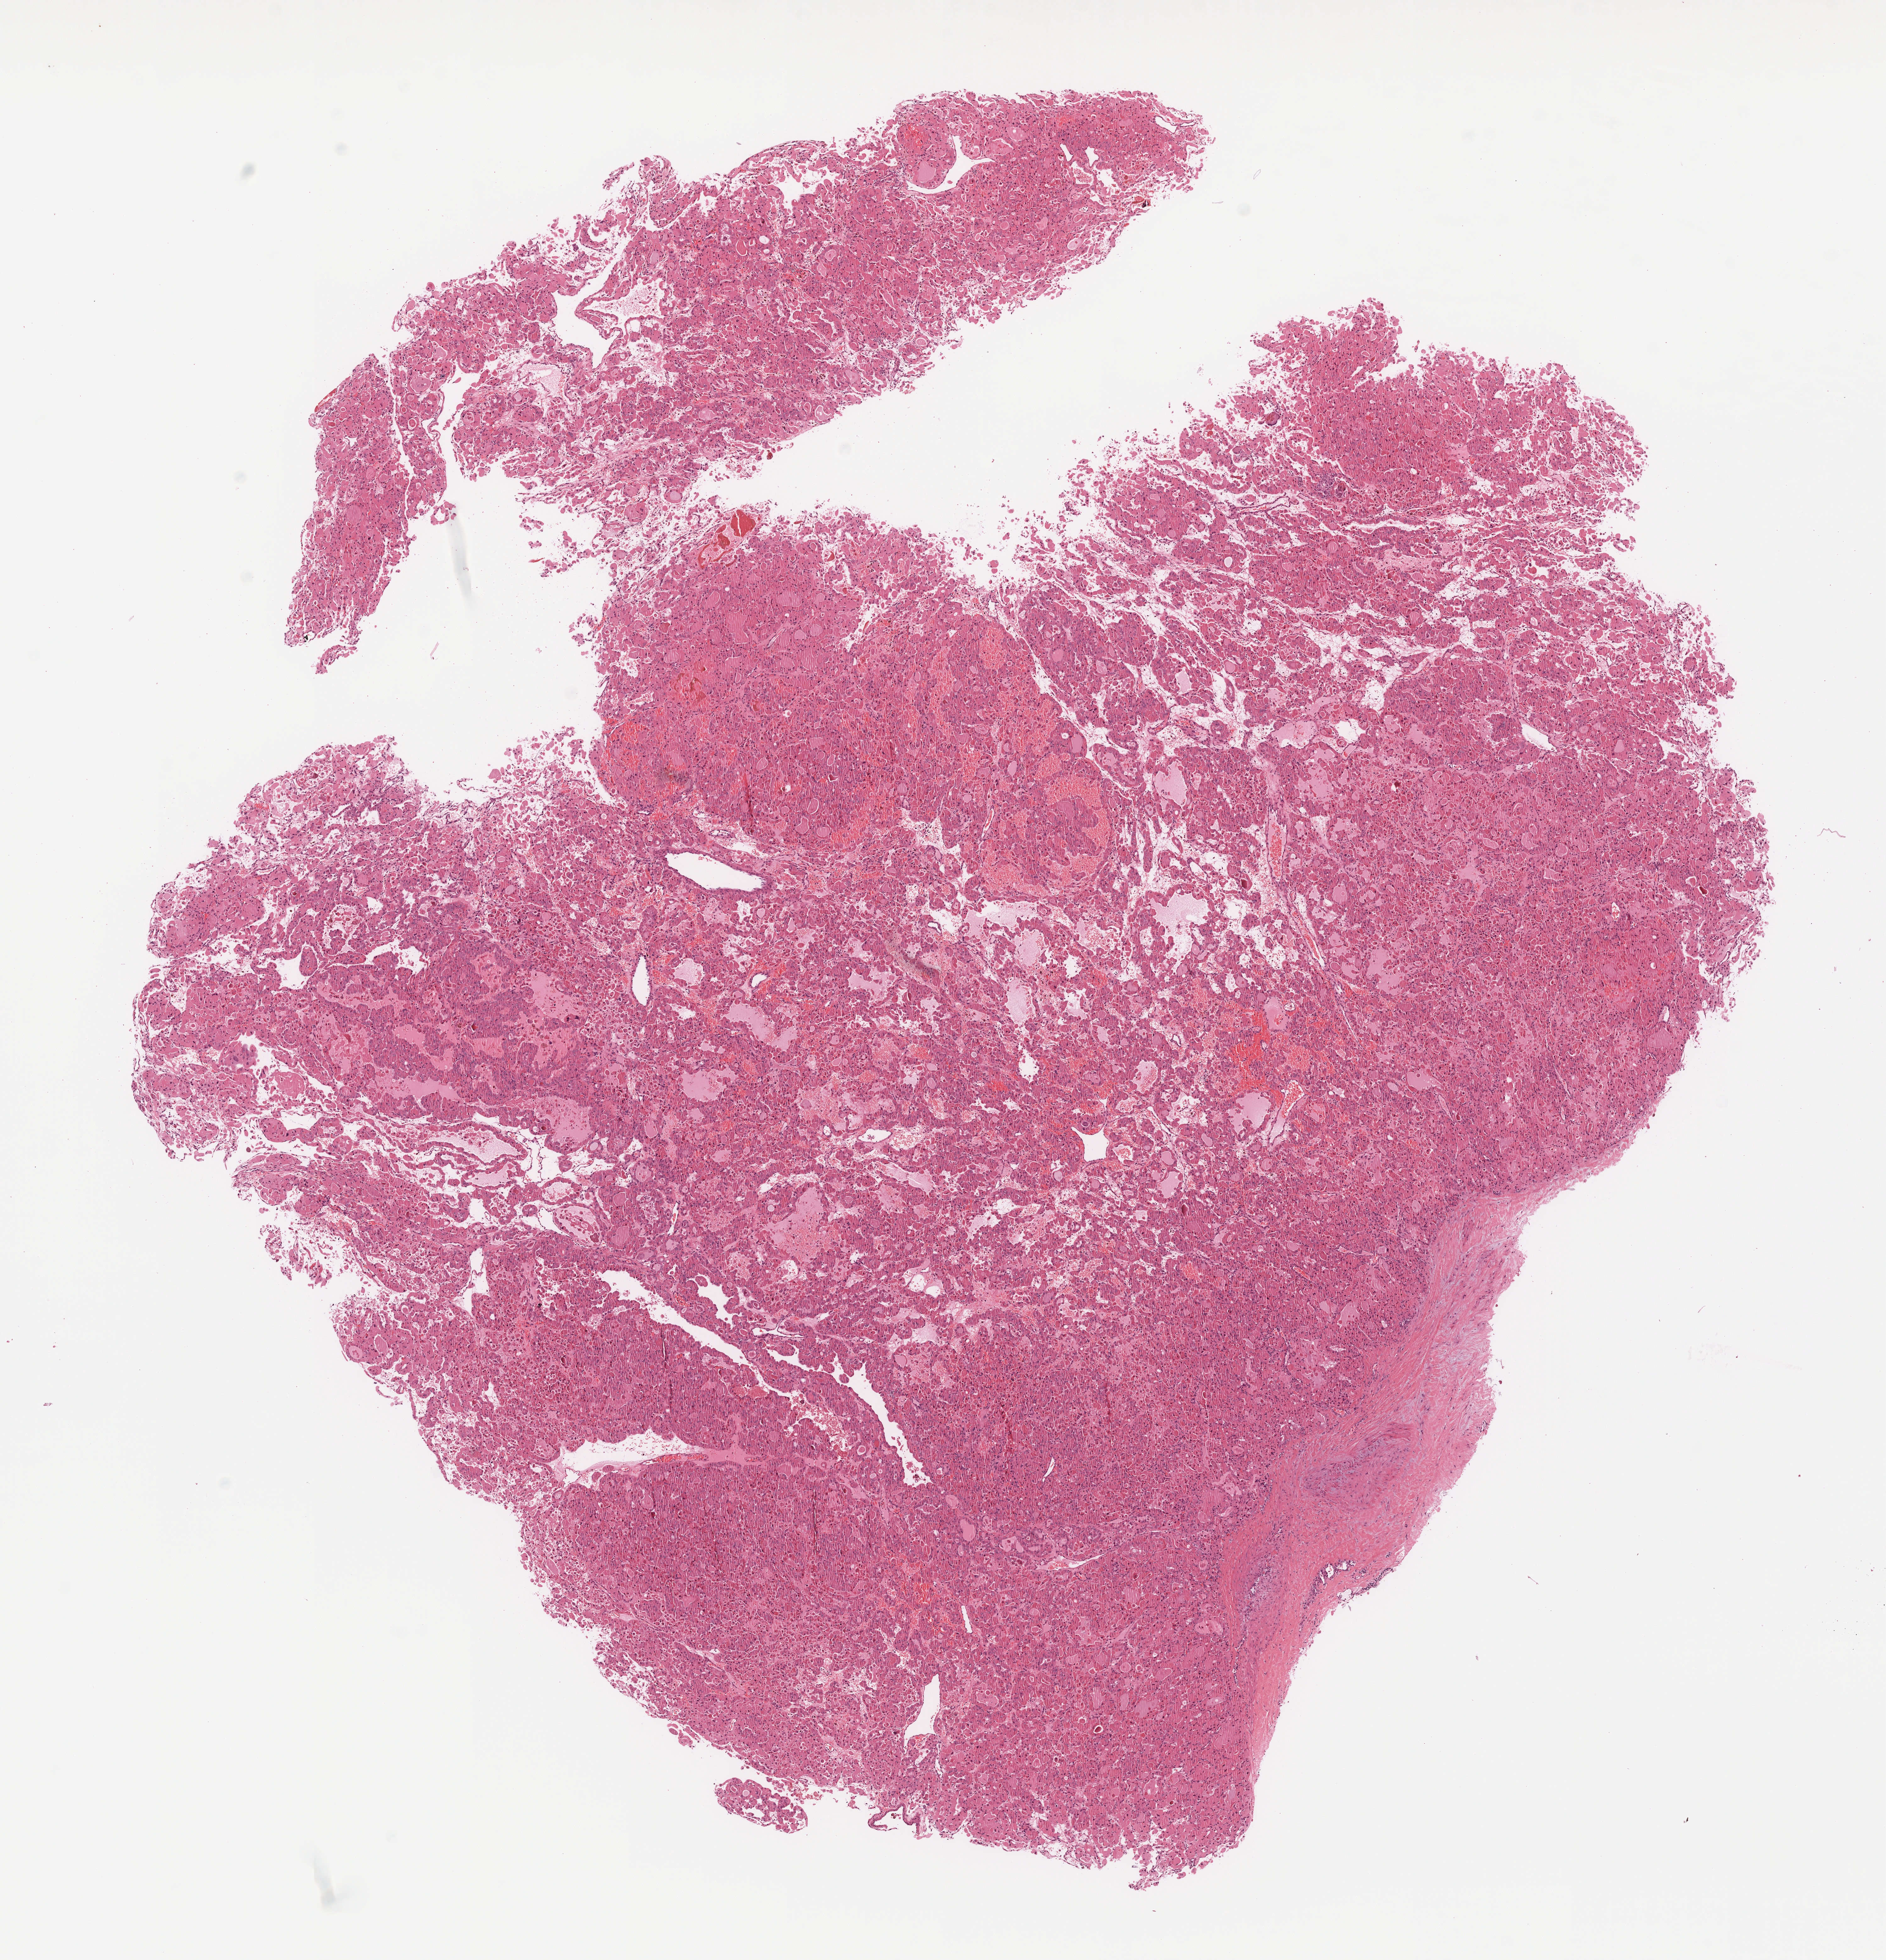
Hematoxylin and eosin (H&E) stained whole-slide image, a low-resolution overview of the entire scanned area, about 12.0 x 12.5 mm (acquisition: 20x scan), formalin-fixed paraffin-embedded (FFPE) diagnostic section, sample: primary tumour, thyroid. Male, age 40 years at initial diagnosis.
Pathologic diagnosis: Papillary carcinoma, follicular variant (thyroid gland). AJCC pathologic stage: I. Lymph nodes positive (case pathology): 0 of 2 examined.